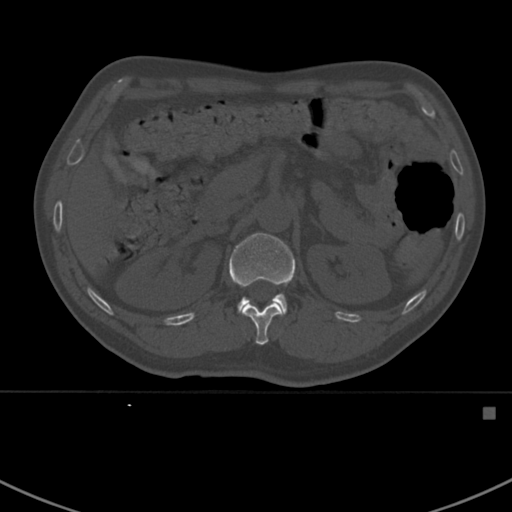
CT including the spine, one axial slice. 120 kVp. Bone window (W 1800 / L 400 HU). 1.5 mm slice thickness. 512 × 512 image matrix, field of view 358 × 358 mm. Patient: male, 59 years. Case-level facts recorded for this patient, not image findings: primary cancer: prostate.
Structures marked on this image (semi-automatically segmented with operator editing):
- L1 vertebra: bounding box <229,233,295,315> (left, top, right, bottom; pixels)
- T12 vertebra: <241,303,282,345>